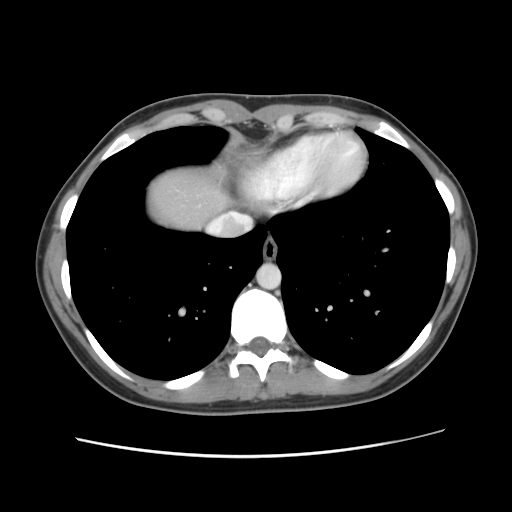
Contrast-enhanced abdominal CT, one axial slice. Slice 117 of 134 in the series (ordered by position). Soft-tissue window (W 400 / L 40 HU). 2.5 mm slice thickness. 512 × 512 image matrix, field of view 339 × 339 mm. Female patient, age 33 years. From the clinical record (not read from this slice): diagnosis: colorectal cancer liver metastases, imaged before liver resection; multiple liver metastases: yes; largest metastasis: 4.5 cm; disease in both lobes: yes.
Structures marked on this image (manually delineated by an expert):
- liver: bounding box [x1, y1, x2, y2] px = [146, 166, 233, 231]
- planned liver remnant (the part of the liver to remain after resection): [146, 166, 233, 231]